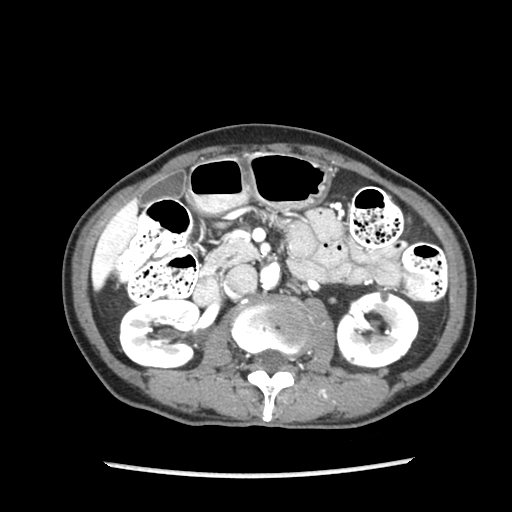
Contrast-enhanced abdominal CT (liver protocol), one axial slice. Slice 37 of 87 in the series (ordered by position). 140 kVp. Soft-tissue window (W 400 / L 40 HU). 2.5 mm slice thickness. 512 × 512 image matrix. Case-level facts recorded for this patient, not image findings: diagnosis: hepatocellular carcinoma (patient treated with transarterial chemoembolisation; whether this scan precedes or follows treatment is not stated here); TNM stage (as recorded): Stage-IIIB; Child-Pugh class: A; tumour differentiation: well differentiated.
Outlined on this slice (semi-automatically segmented with operator editing):
- liver parenchyma outside the tumour (the mass and vessels are separate outlines, so this box may not span the whole liver): box from (x=92, y=198) to (x=138, y=289) px
- liver vessels: (x=99, y=212)–(x=127, y=275)